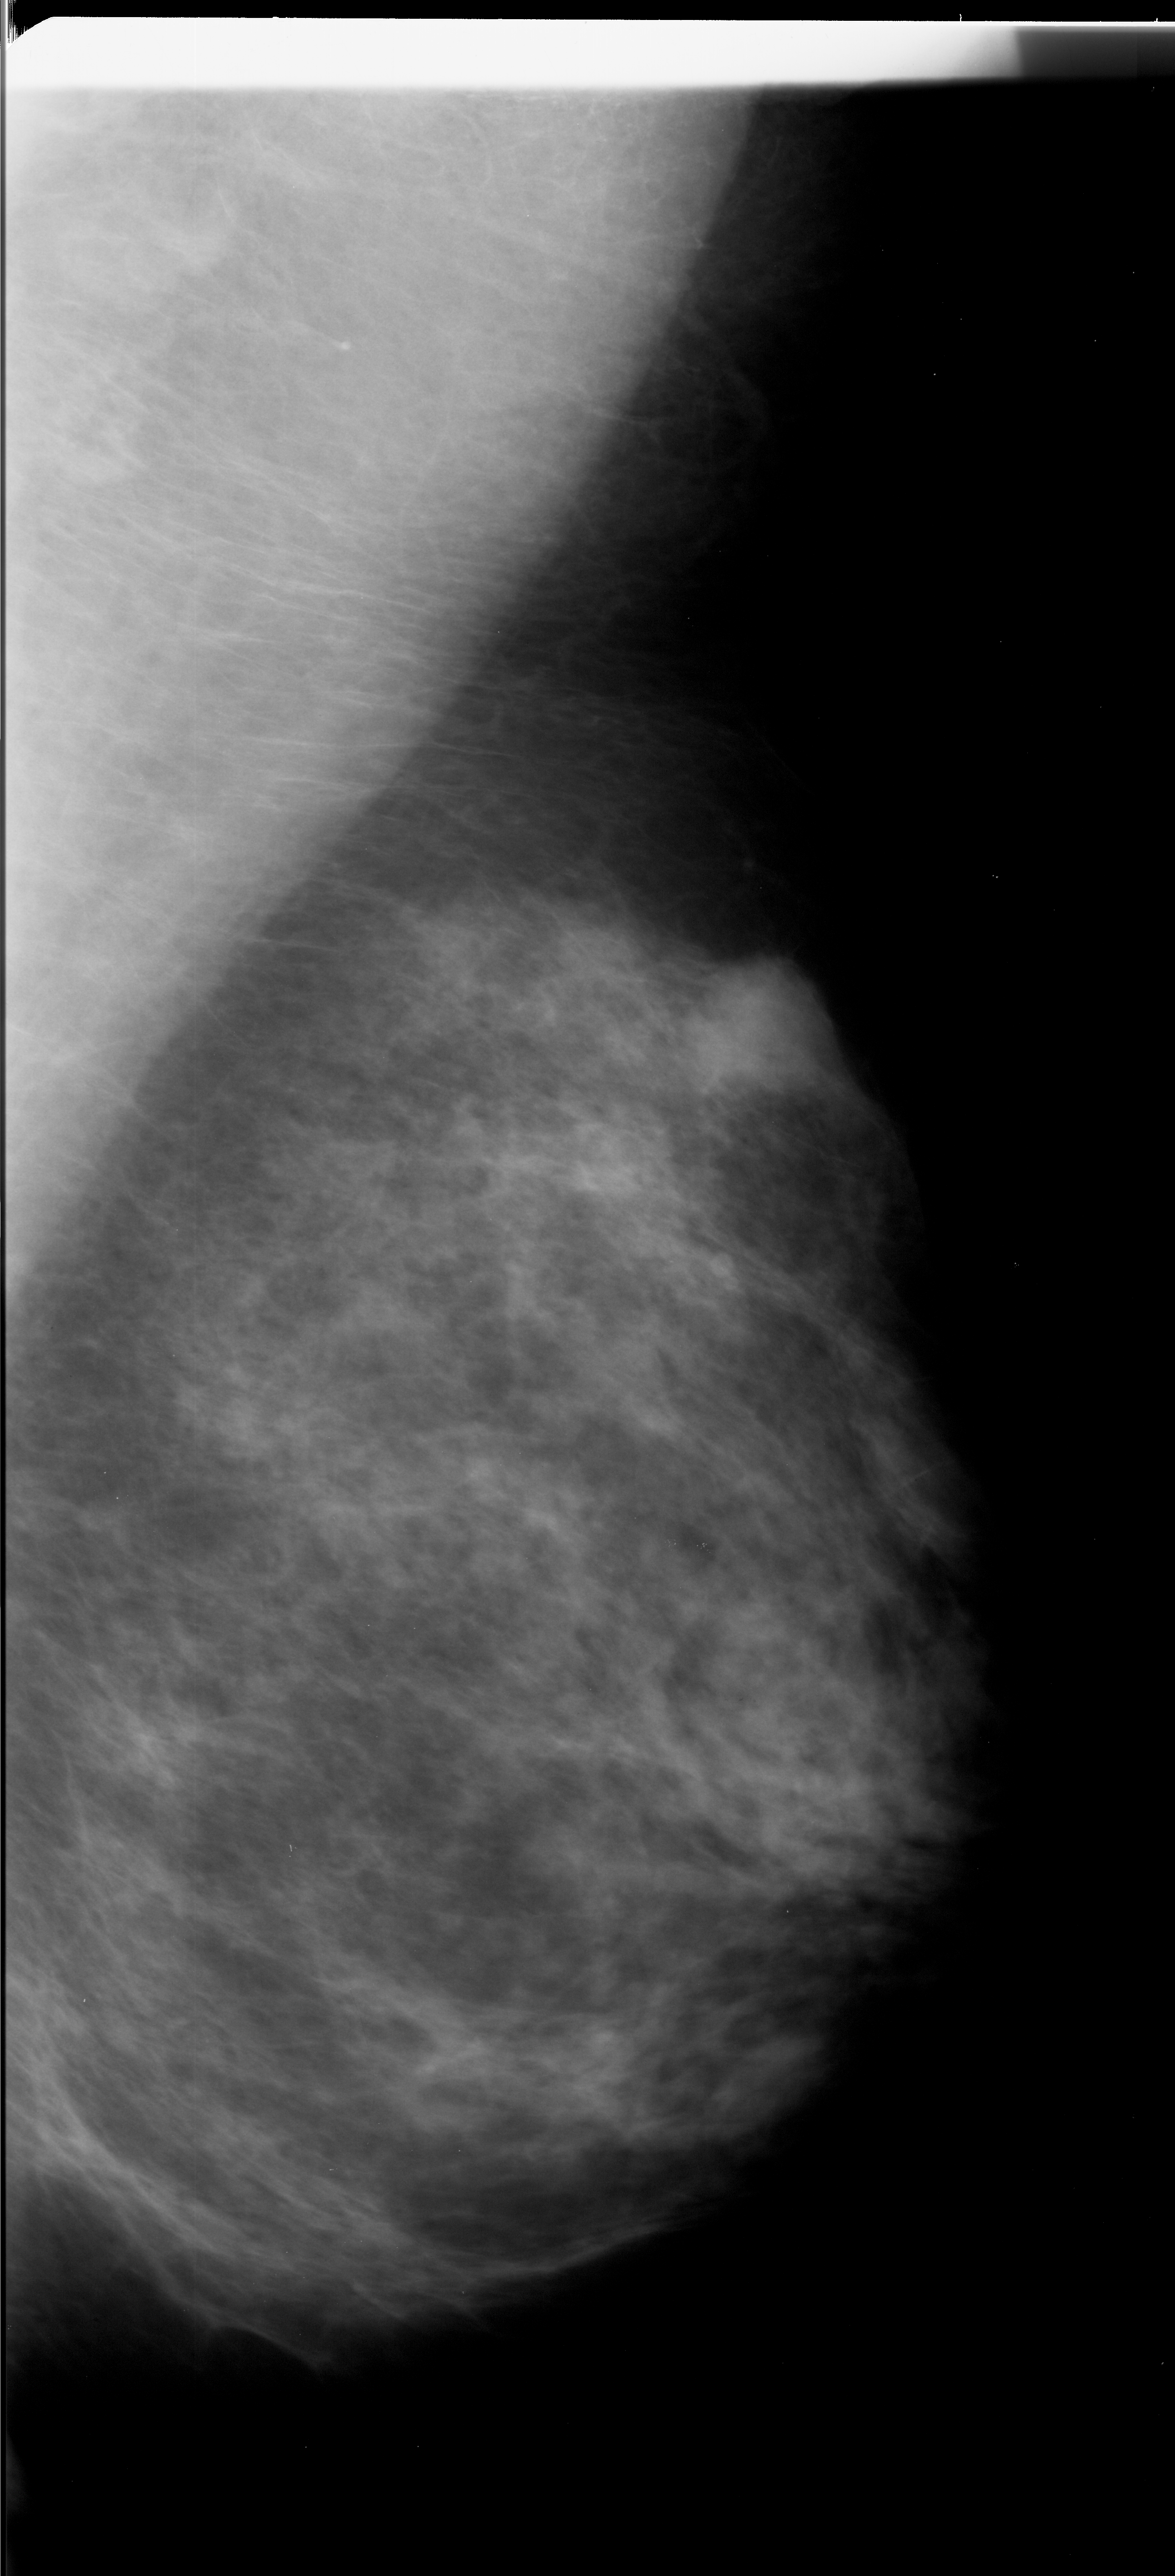
Scanned film-screen mammogram. Right breast. MLO view. Breast composition: heterogeneously dense (BI-RADS density category 3 of 4). 1175 × 2576 image matrix.
Marked abnormalities (boxes around the expert regions of interest):
- mass, shape irregular, margins ill defined; BI-RADS assessment category 4; pathology result (as recorded, not read from the image): malignant: bounding box (x1, y1, x2, y2) in pixels: (688, 940, 843, 1087)